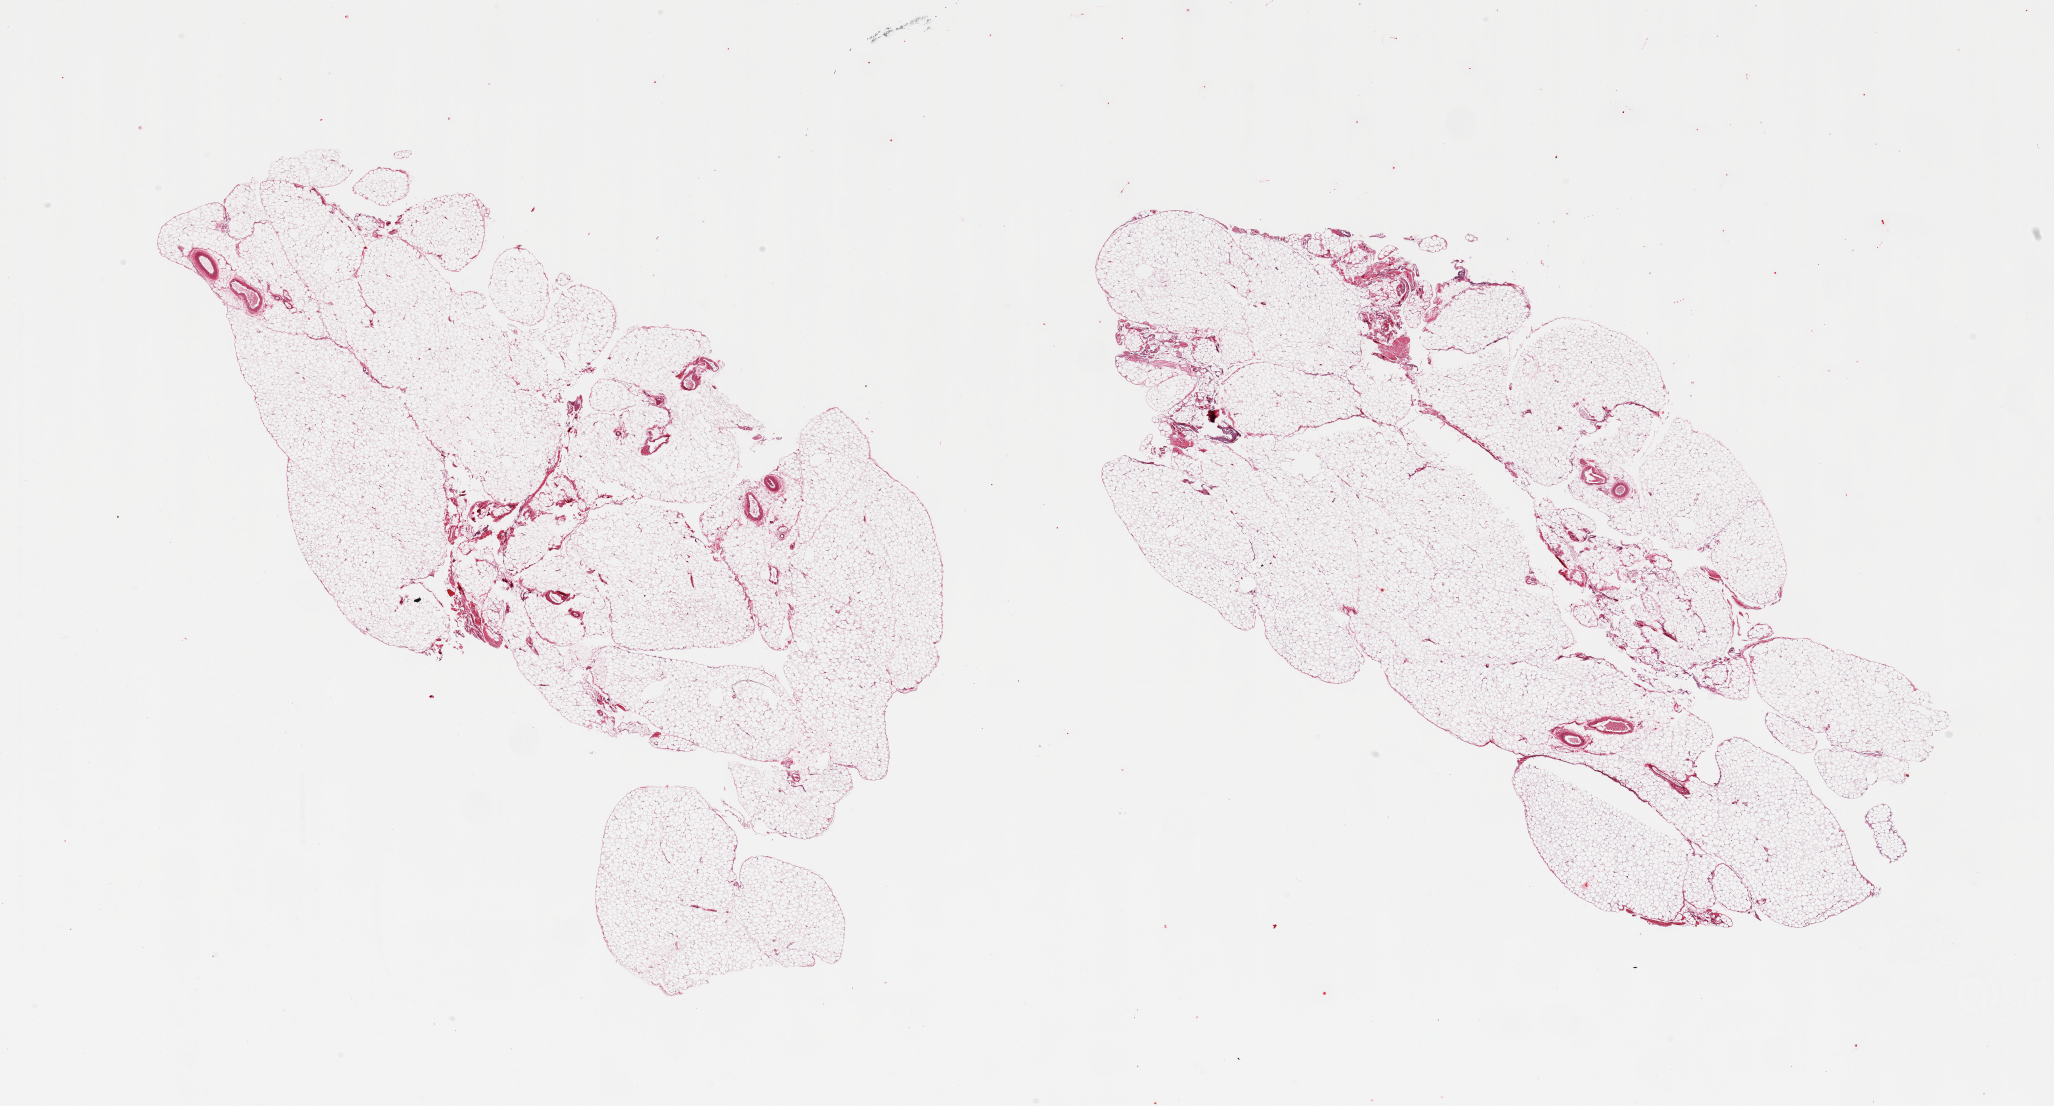
Haematoxylin and eosin whole-slide image, whole scanned area (about 32.5 x 17.5 mm) shown as a low-resolution overview, PAXgene-fixed, paraffin-embedded tissue, target tissue: omentum, tissue donor sample. Donor sex: male.
Pathologist's review note for this sample: 2 pieces, minimal fascia.